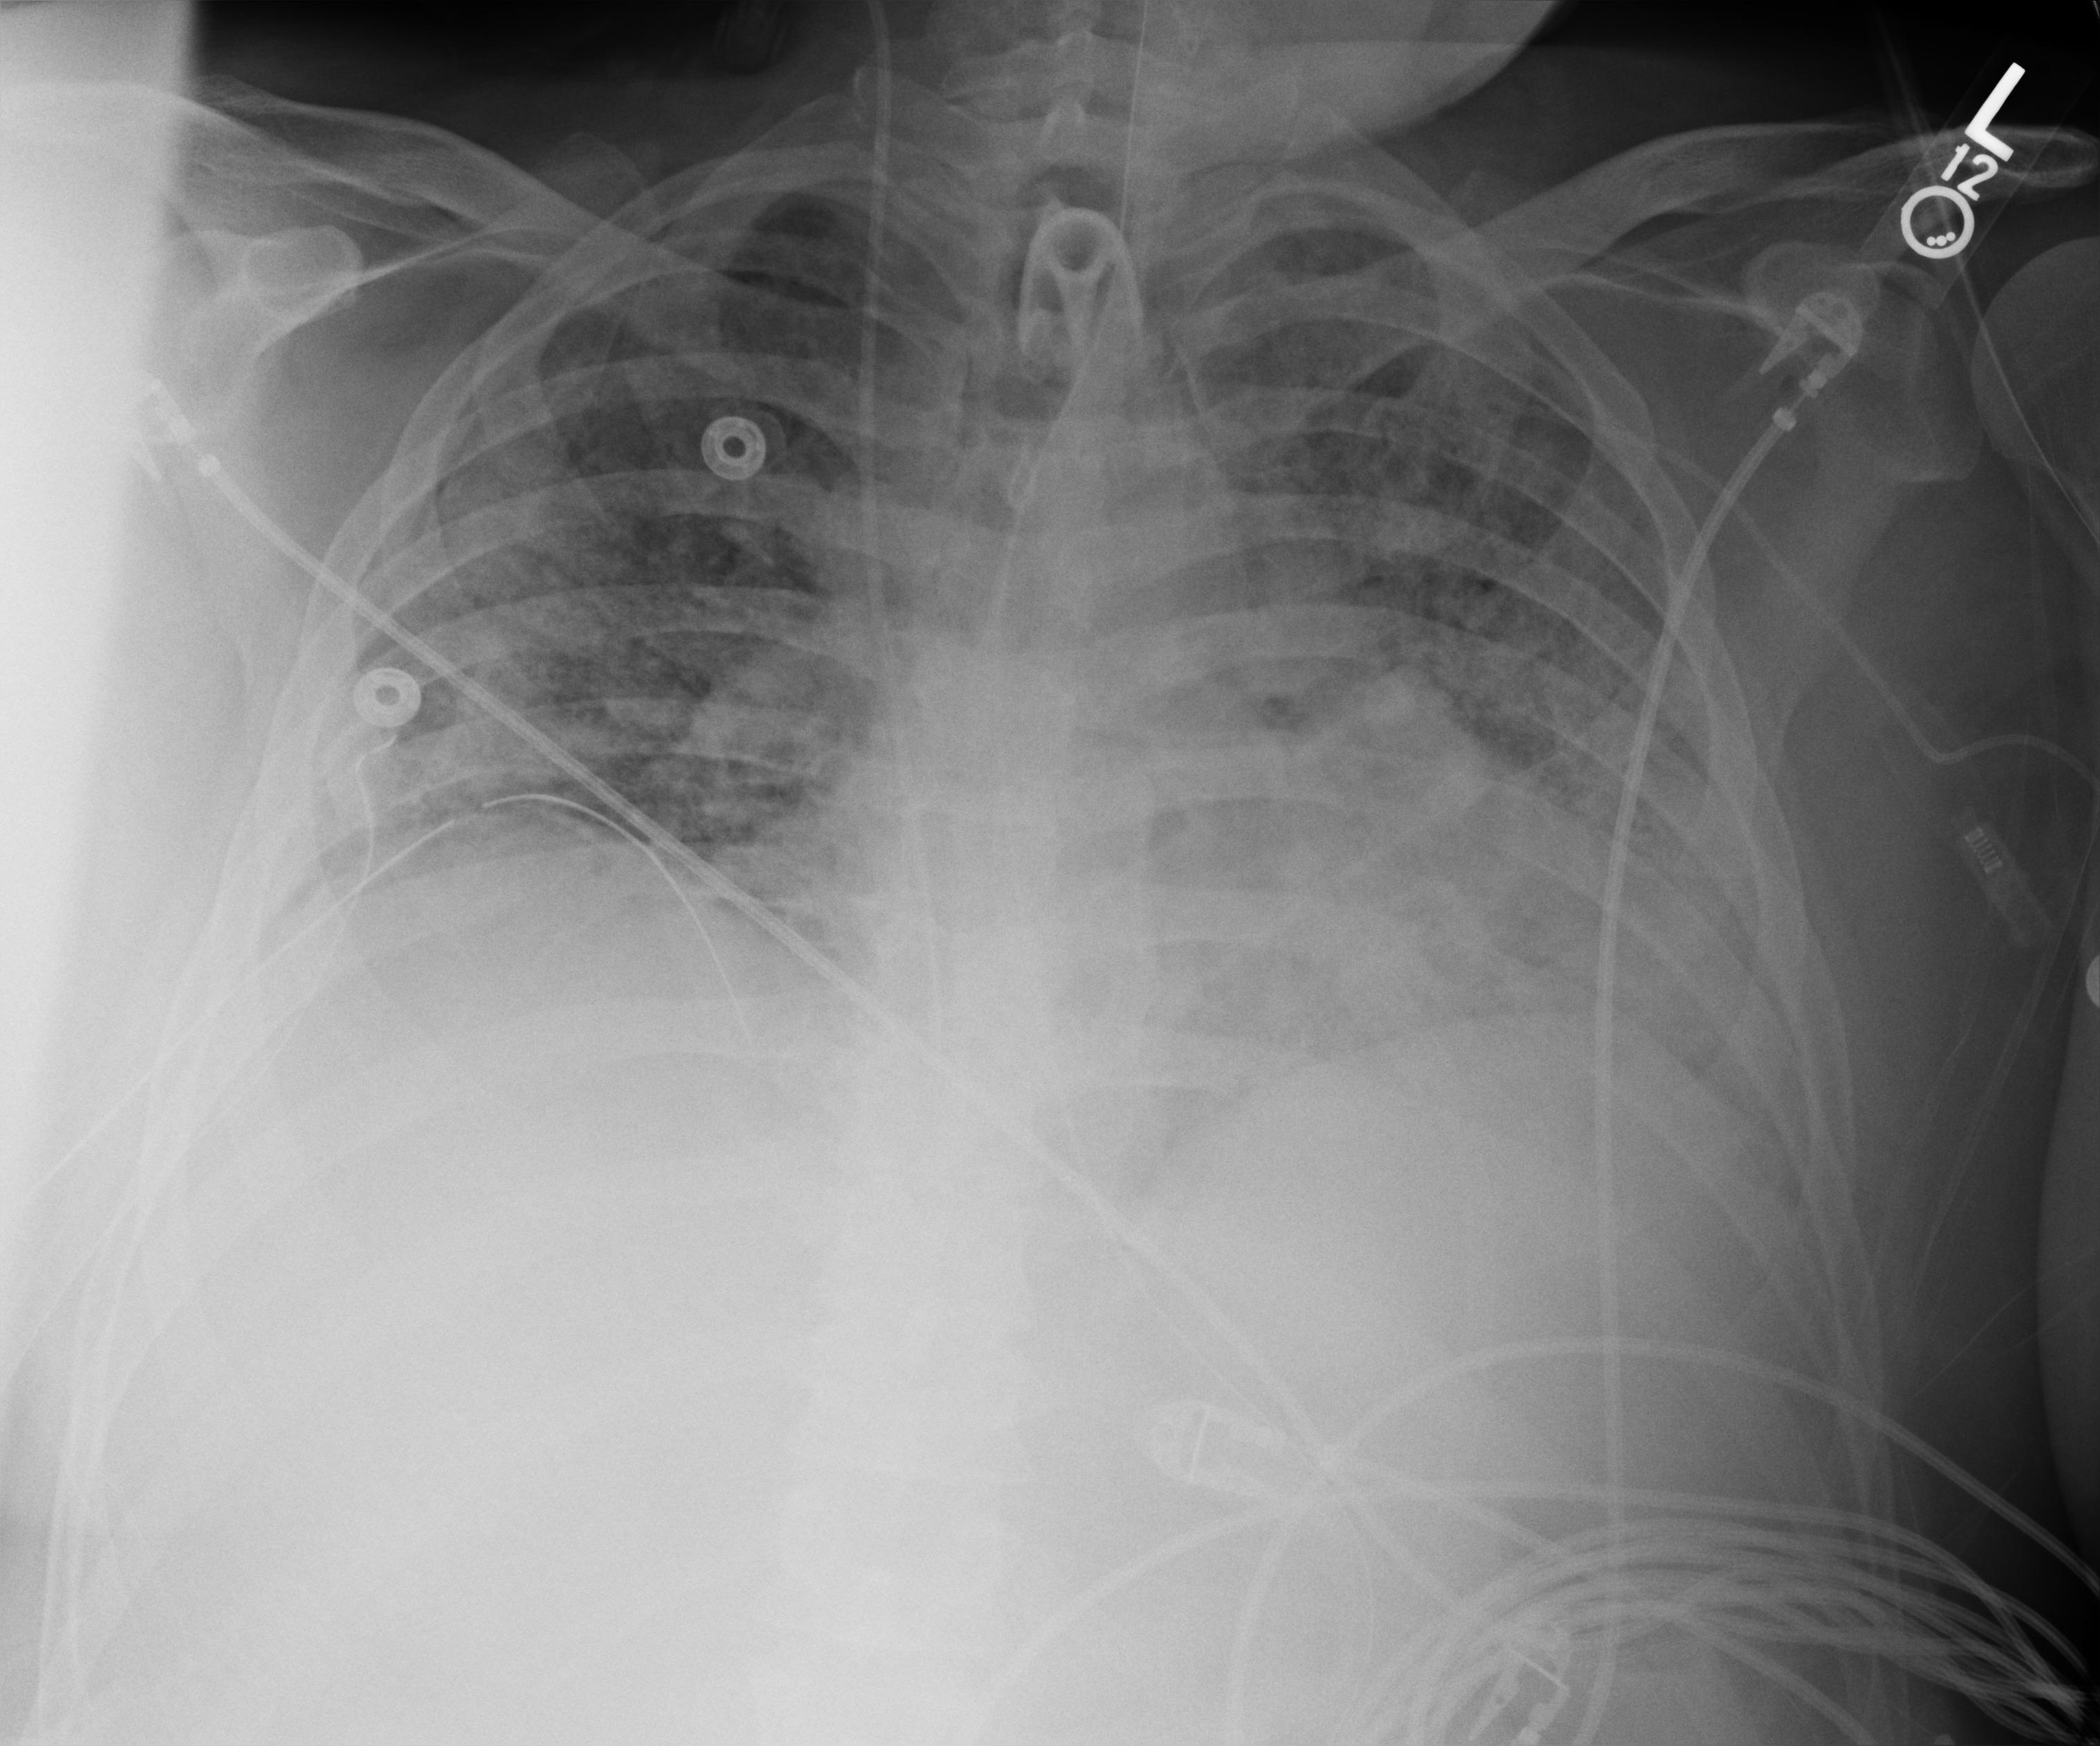
Bedside chest radiograph (computed radiography); anteroposterior (AP) projection. Patient hospitalised with COVID-19; male, aged 18–59 years.
Admission-level facts for this patient (not findings on this image; timing relative to this image not recorded): mechanically ventilated during this hospital stay: yes; length of hospital stay: 80 days.